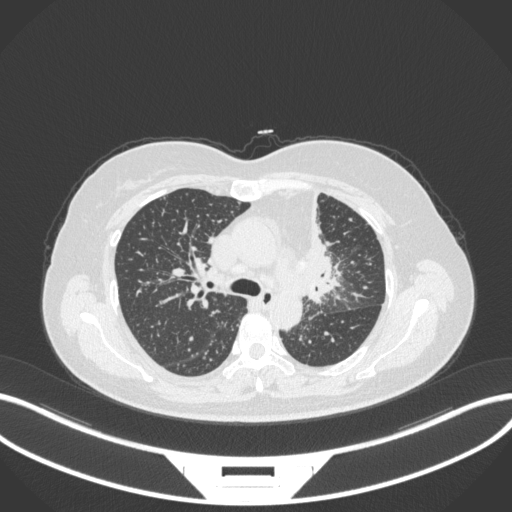
Chest CT, one axial slice; slice 223 of 348 in the series (ordered by position); reconstruction kernel B31f; 120 kVp; lung window (W 1500 / L -600 HU); 1 mm slice thickness; 512 × 512 image matrix, field of view 400 × 400 mm. Female patient, age 49 years. Case-level facts recorded for this patient, not image findings: clinical TNM (as recorded): T1c N0 M1.
Annotated regions visible in this slice (bounding box drawn by a radiologist):
- lung tumour (recorded histology: adenocarcinoma): bounding box <296,187,347,308> (left, top, right, bottom; pixels)